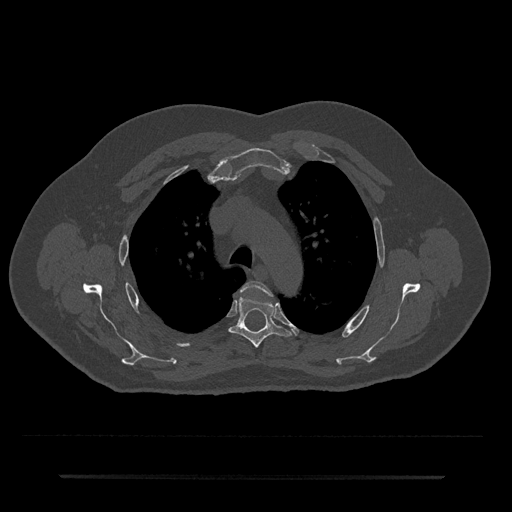
CT including the spine, one axial slice. Slice 532 of 797 in the series (ordered by position). Bone window (W 1800 / L 400 HU). 0.5 mm slice thickness. 512 × 512 image matrix, field of view 437 × 437 mm. Patient: male, 69 years. From the clinical record (not read from this slice): primary cancer: prostate.
Outlined on this slice (semi-automatically segmented with operator editing):
- T3 vertebra: bounding box <242,281,272,296> (left, top, right, bottom; pixels)
- T4 vertebra: <229,297,290,348>